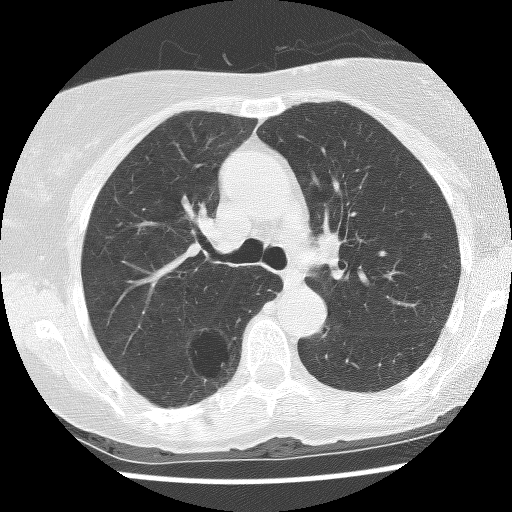
Low-dose screening chest CT, axial slice, first (baseline) screen, lung window (W 1500 / L -600 HU), 2.5 mm slice thickness, slice 43 of 136 in the series. Female, age 69 years at enrolment. Former smoker at enrolment.
Expert reader's lesion annotation, bounding box (x1, y1, x2, y2) in pixels: (170, 323, 244, 396). The screening reader recorded 2 non-calcified nodules or masses ≥4 mm on this exam (right lower lobe, right lower lobe); which of them this box marks is not recorded. Official screen result: positive, change unspecified: nodule(s) >= 4 mm or enlarging nodule(s), mass(es), or other non-specific abnormalities suspicious for lung cancer. Later outcome: lung cancer diagnosed 288 days after this screen — non-small cell carcinoma, right lower lobe, poorly differentiated (G3), stage IB (AJCC 6th edition), 36 mm at pathology.